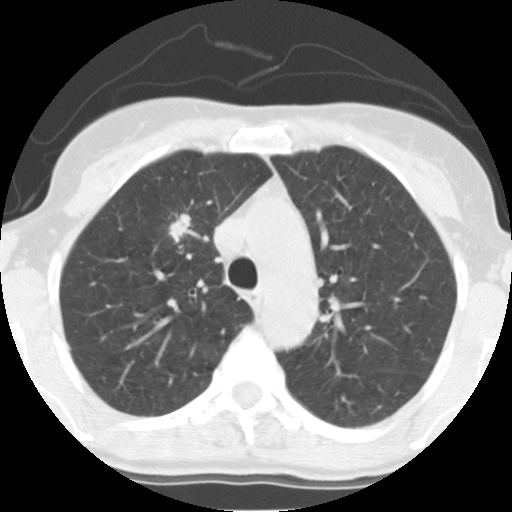
Low-dose screening chest CT, one axial slice. Position 100 of 140 along the scan axis. Reconstruction kernel STANDARD. 140 kVp. Lung window (W 1500 / L -600 HU). 2.5 mm slice thickness. 512 × 512 image matrix, field of view 280 × 280 mm.
Annotated regions visible in this slice (expert manual segmentation):
- lesion 1 (tumor, upper lobe of right lung): box from (x=168, y=214) to (x=192, y=242) px